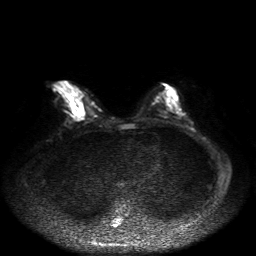
Breast MRI, one axial slice. Slice 23 of 50 in the series (ordered by position). Diffusion-weighted series; image 2 of 4 stored at this slice position (different b-values; order by instance number). 1.5 T. 4 mm slice thickness. 256 × 256 image matrix. Female patient.
Annotated regions visible in this slice (expert manual segmentation):
- tumour on diffusion-weighted imaging: bounding box (x1, y1, x2, y2) in pixels: (75, 107, 81, 110)